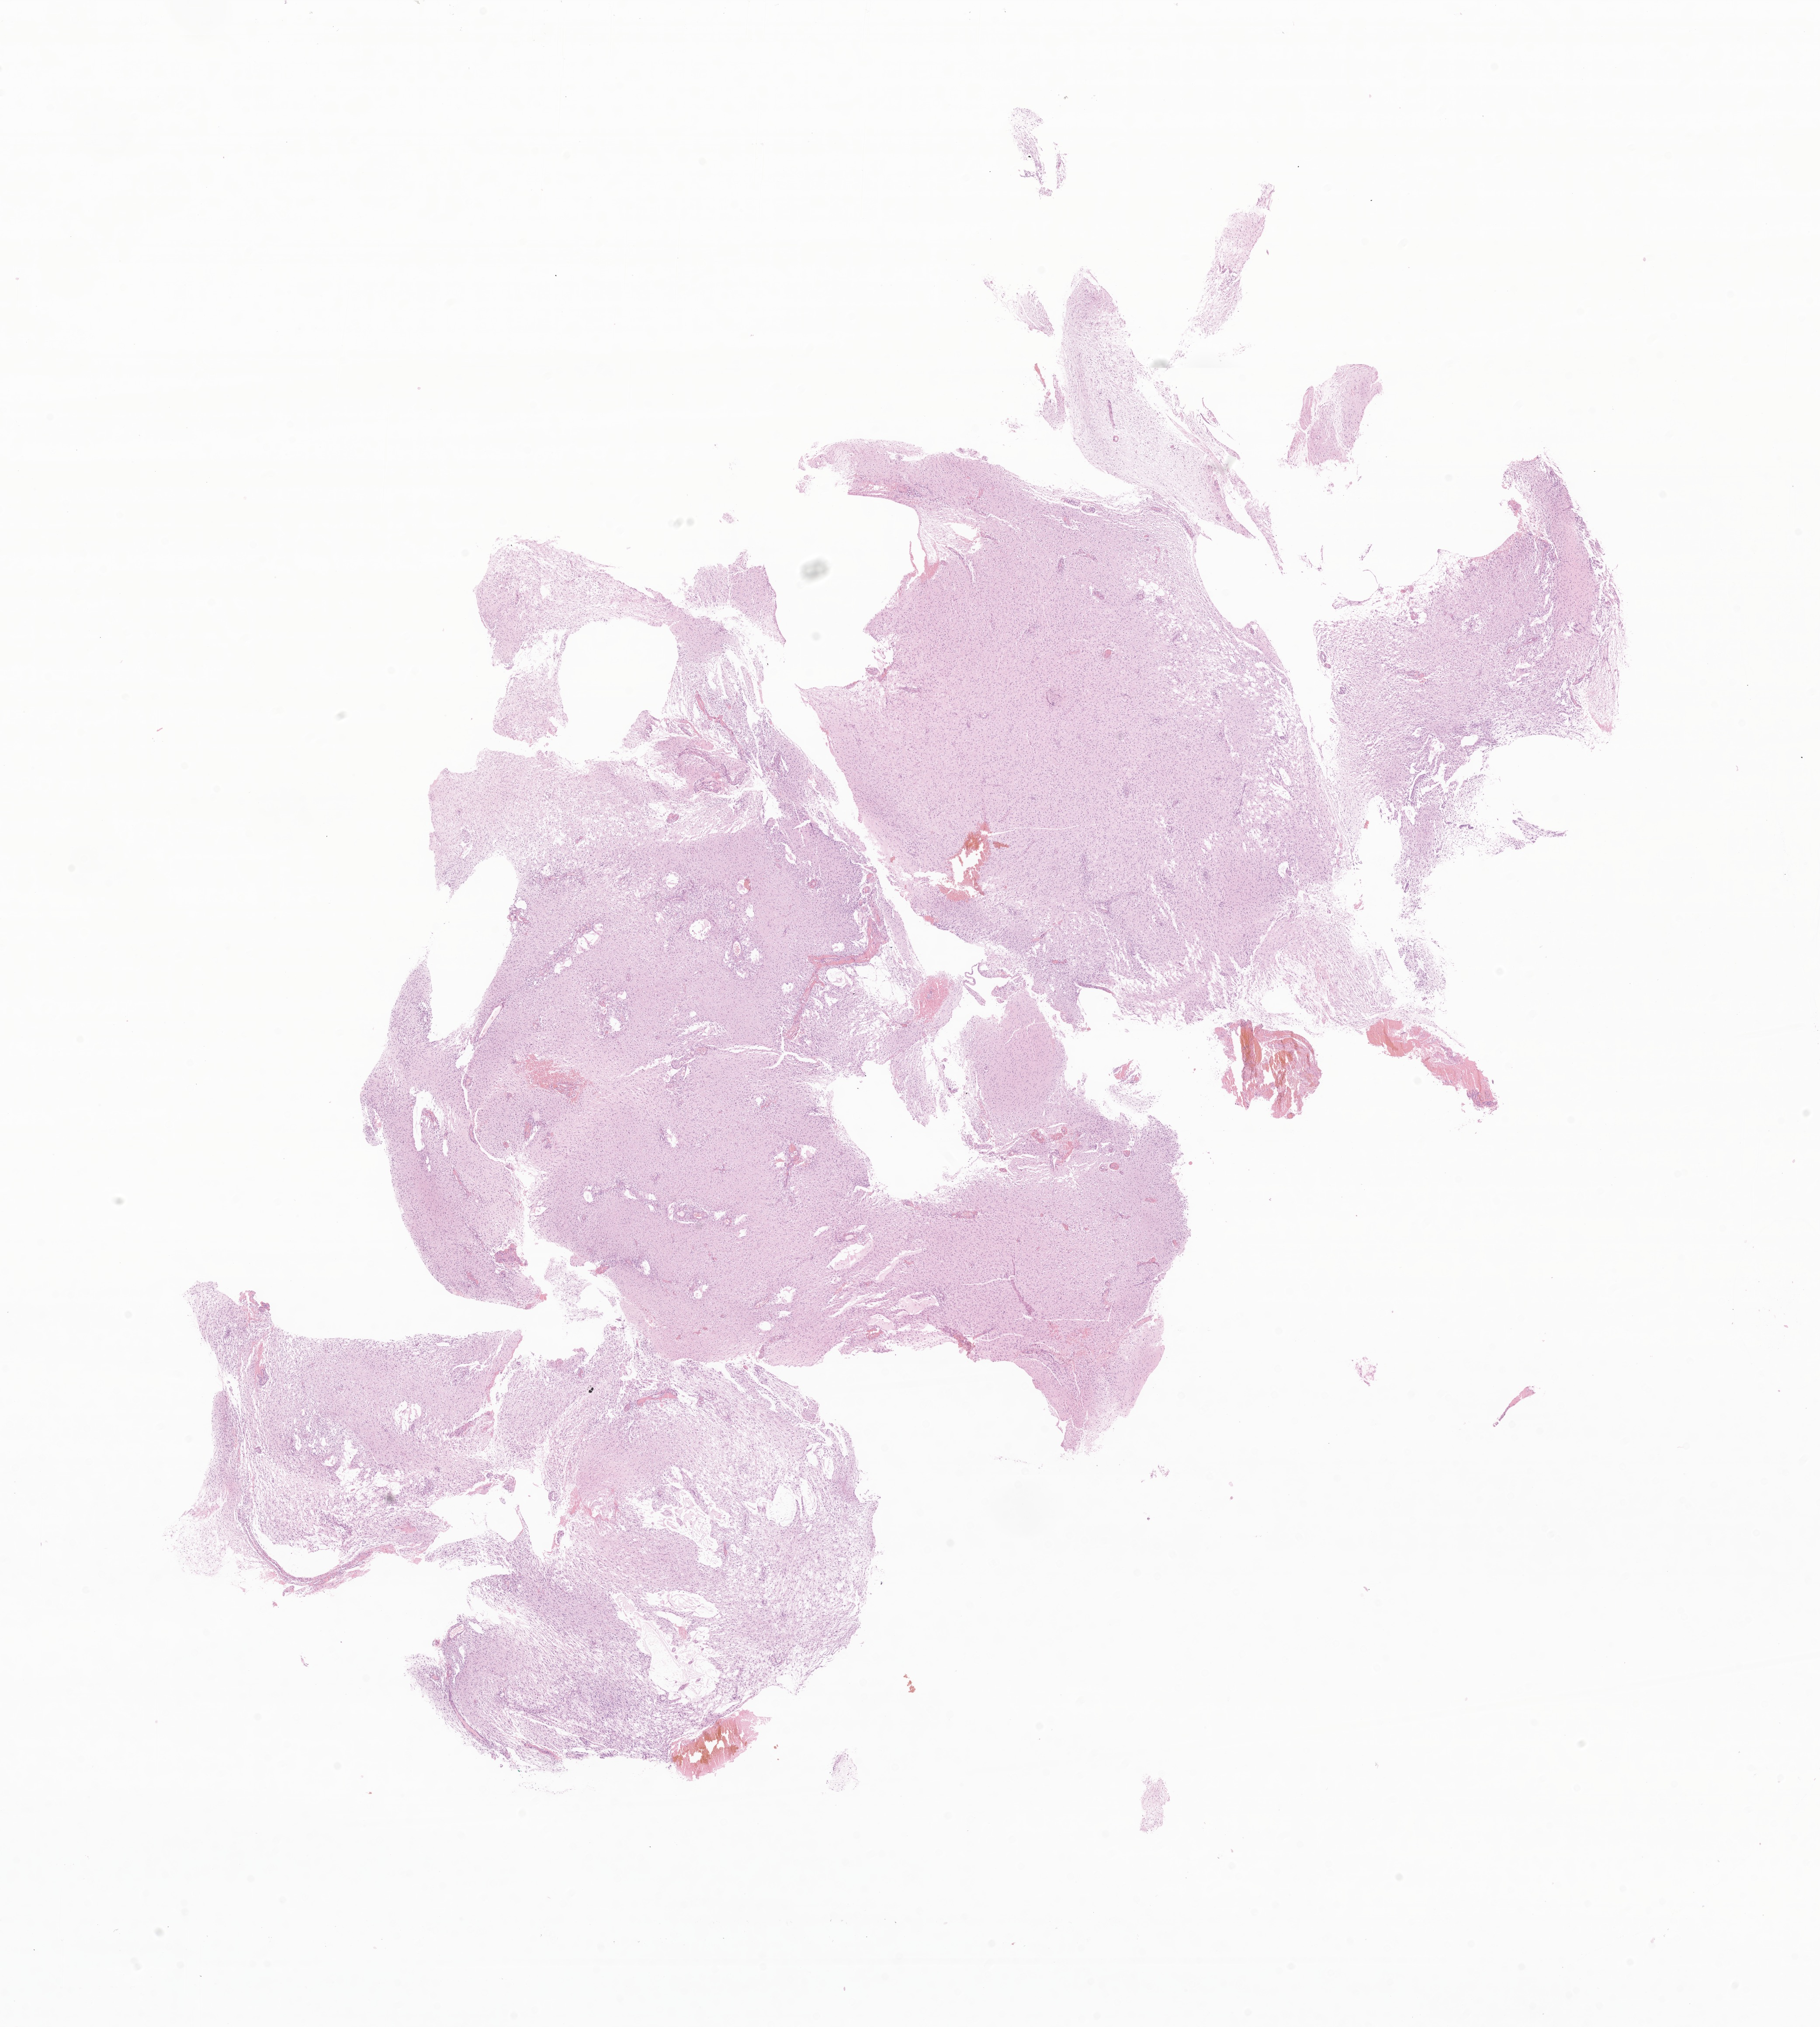
Haematoxylin and eosin whole-slide image of tumor tissue from the brain — whole scanned area (about 17.6 x 19.6 mm) shown as a low-resolution overview. FFPE section. Patient female; age 89 months (7 years 5 months).
- diagnosis: Glioma, malignant